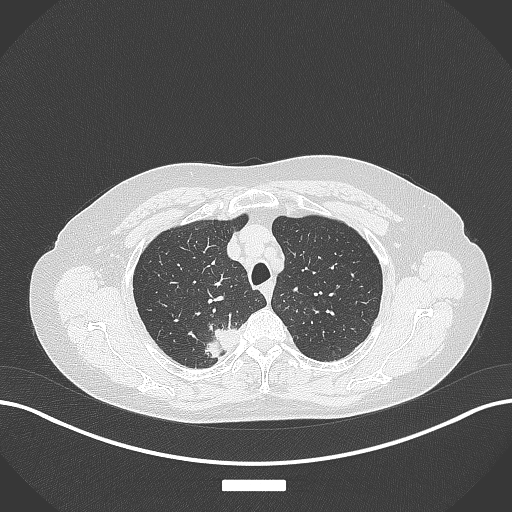
Chest CT, one axial slice; slice 316 of 357 in the series (ordered by position); lung window (W 1500 / L -600 HU); 1 mm slice thickness; 512 × 512 image matrix. Patient: female, 62 years. From the clinical record (not read from this slice): clinical TNM (as recorded): T1c N1 M0.
Annotated regions visible in this slice (bounding box drawn by a radiologist):
- lung tumour (recorded histology: squamous cell carcinoma): bounding box (x1, y1, x2, y2) in pixels: (199, 320, 244, 360)